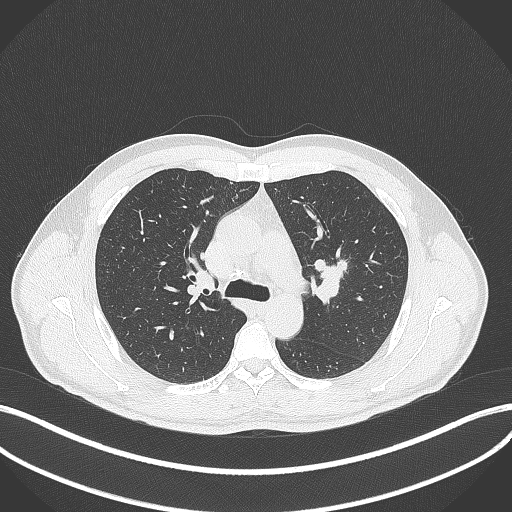
Chest CT, one axial slice. Reconstruction kernel B70f. 120 kVp. Lung window (W 1500 / L -600 HU). 512 × 512 image matrix, field of view 400 × 400 mm. Patient: male, 50 years. From the clinical record (not read from this slice): clinical TNM (as recorded): T1c N1 M1b.
Annotated regions visible in this slice (bounding box drawn by a radiologist):
- lung tumour (recorded histology: squamous cell carcinoma): bounding box [x1, y1, x2, y2] px = [310, 256, 350, 306]